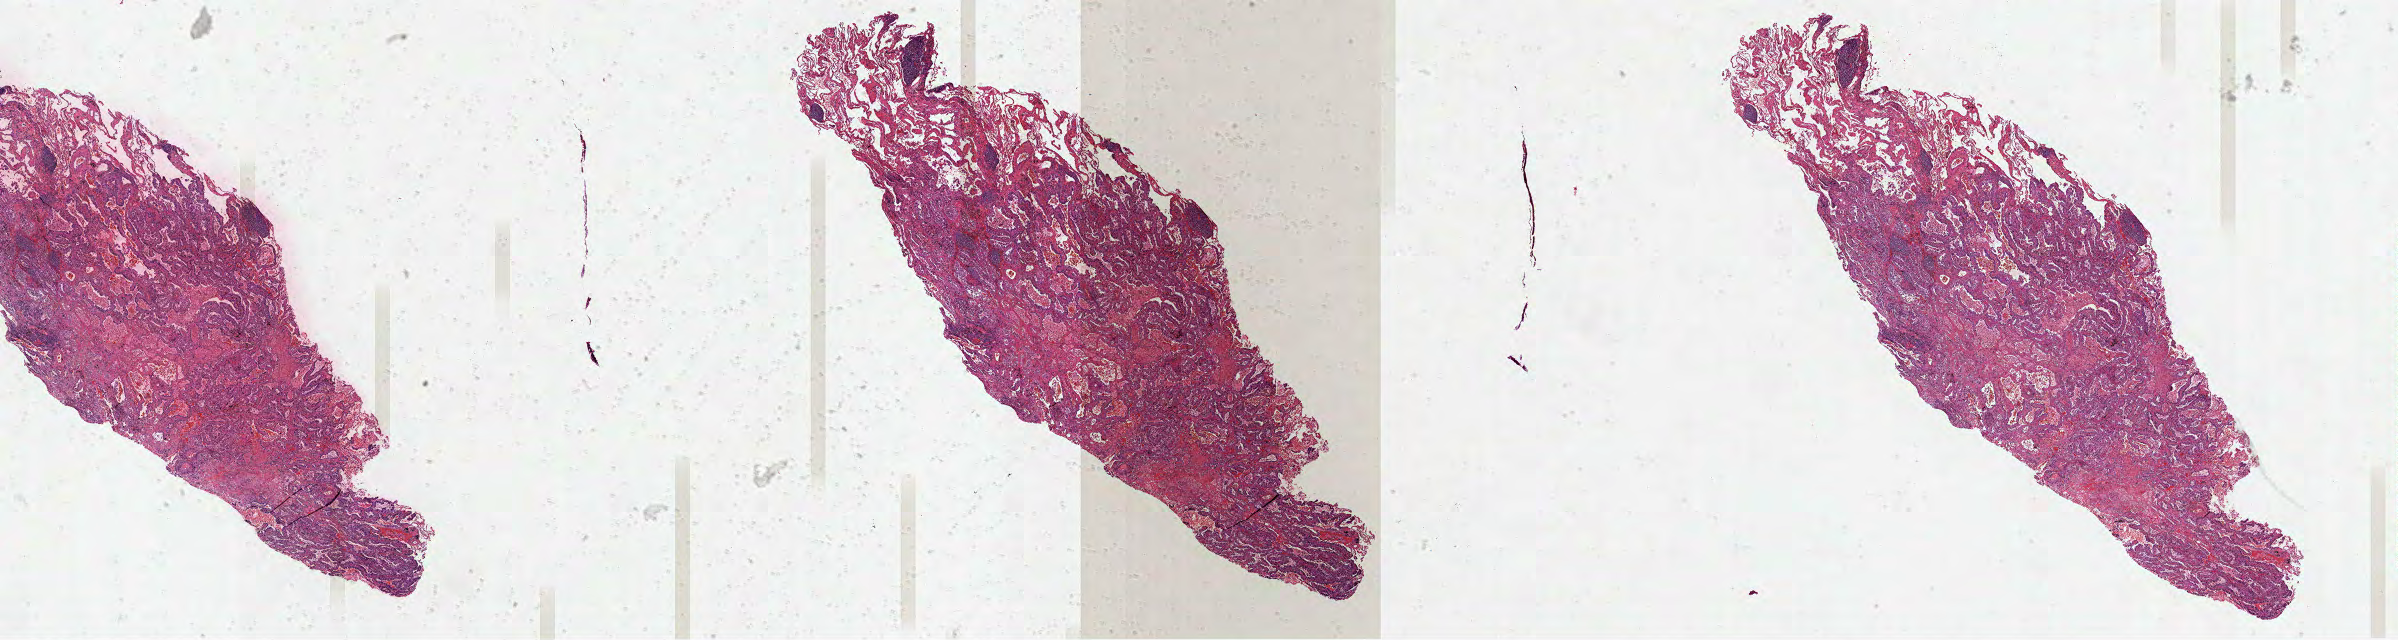
Whole-slide histology image, Hematoxylin and eosin (H&E) stained, whole scanned area (about 38.7 x 10.3 mm) shown as a low-resolution overview; formalin-fixed paraffin-embedded (FFPE) diagnostic section; sample: primary tumour, lung. Female, age 47 years at initial diagnosis.
* pathologic diagnosis: Adenocarcinoma, NOS (upper lobe, lung)
* AJCC pathologic stage: IIA (7th edition)
* laterality: left